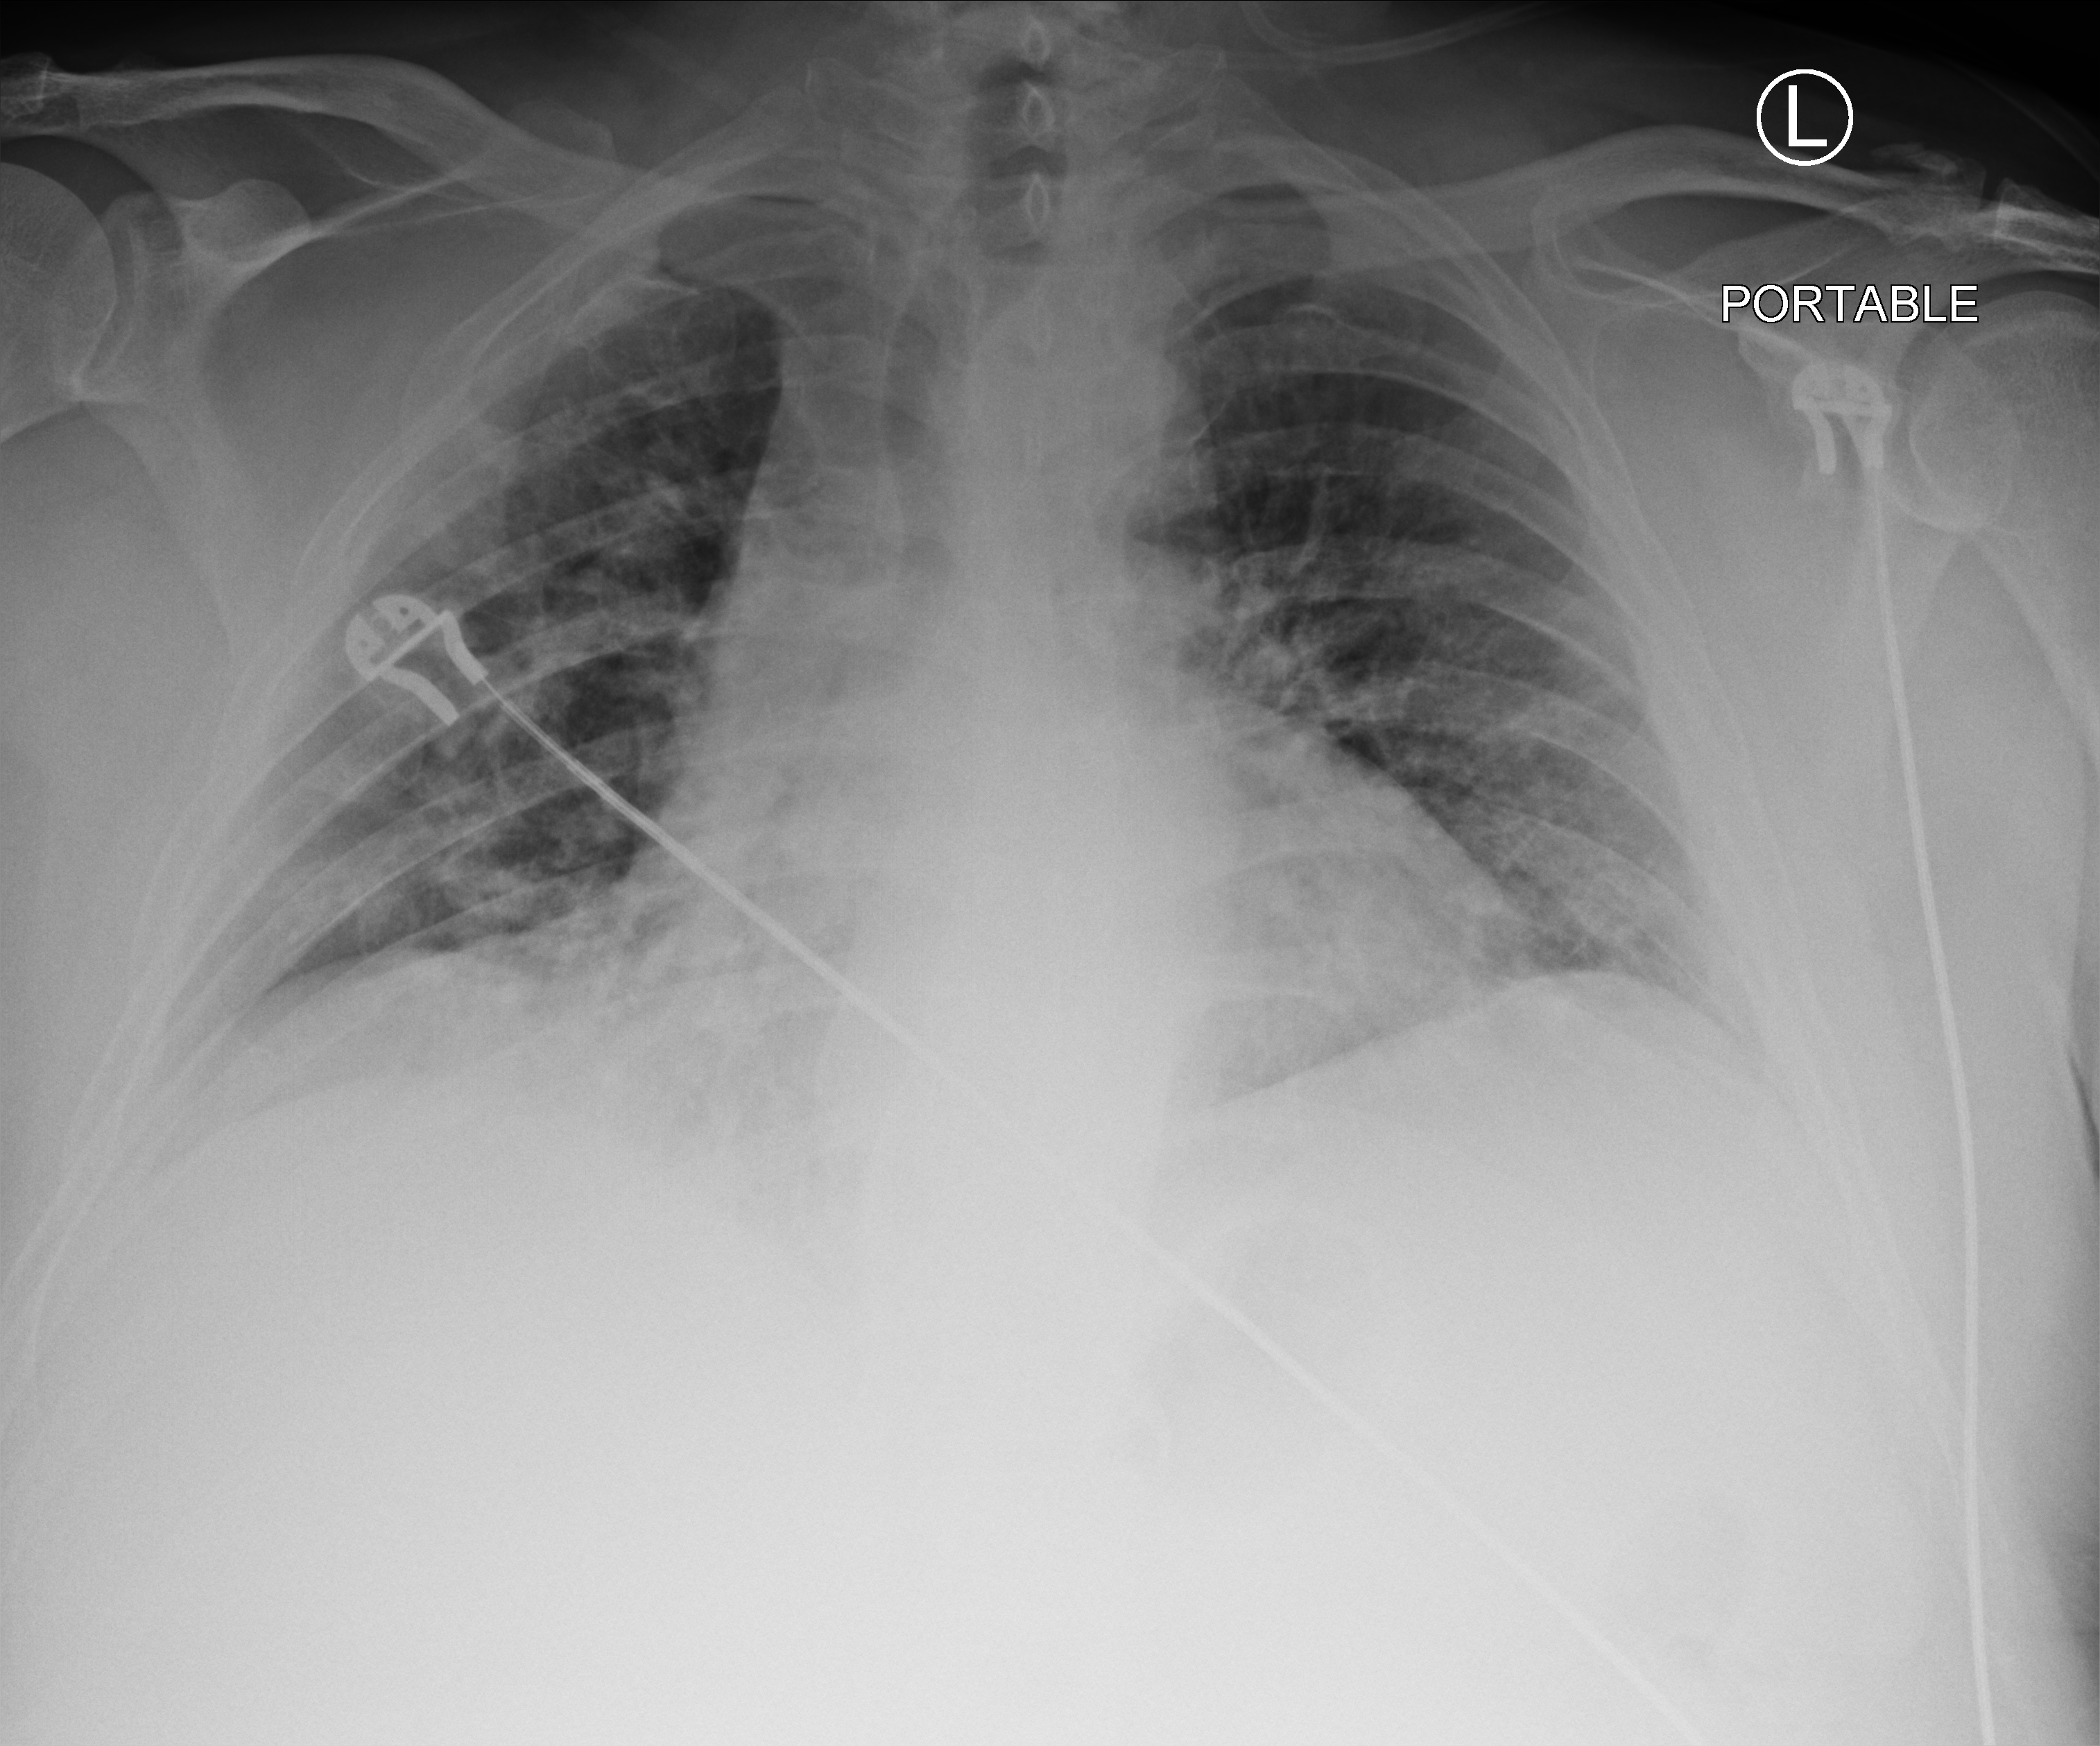
Chest X-ray (portable), anteroposterior (AP) projection. Male patient hospitalised with COVID-19, age 18–59 years.
Admission-level facts for this patient (not findings on this image; timing relative to this image not recorded):
- admitted to intensive care during this hospital stay: no
- mechanically ventilated during this hospital stay: no